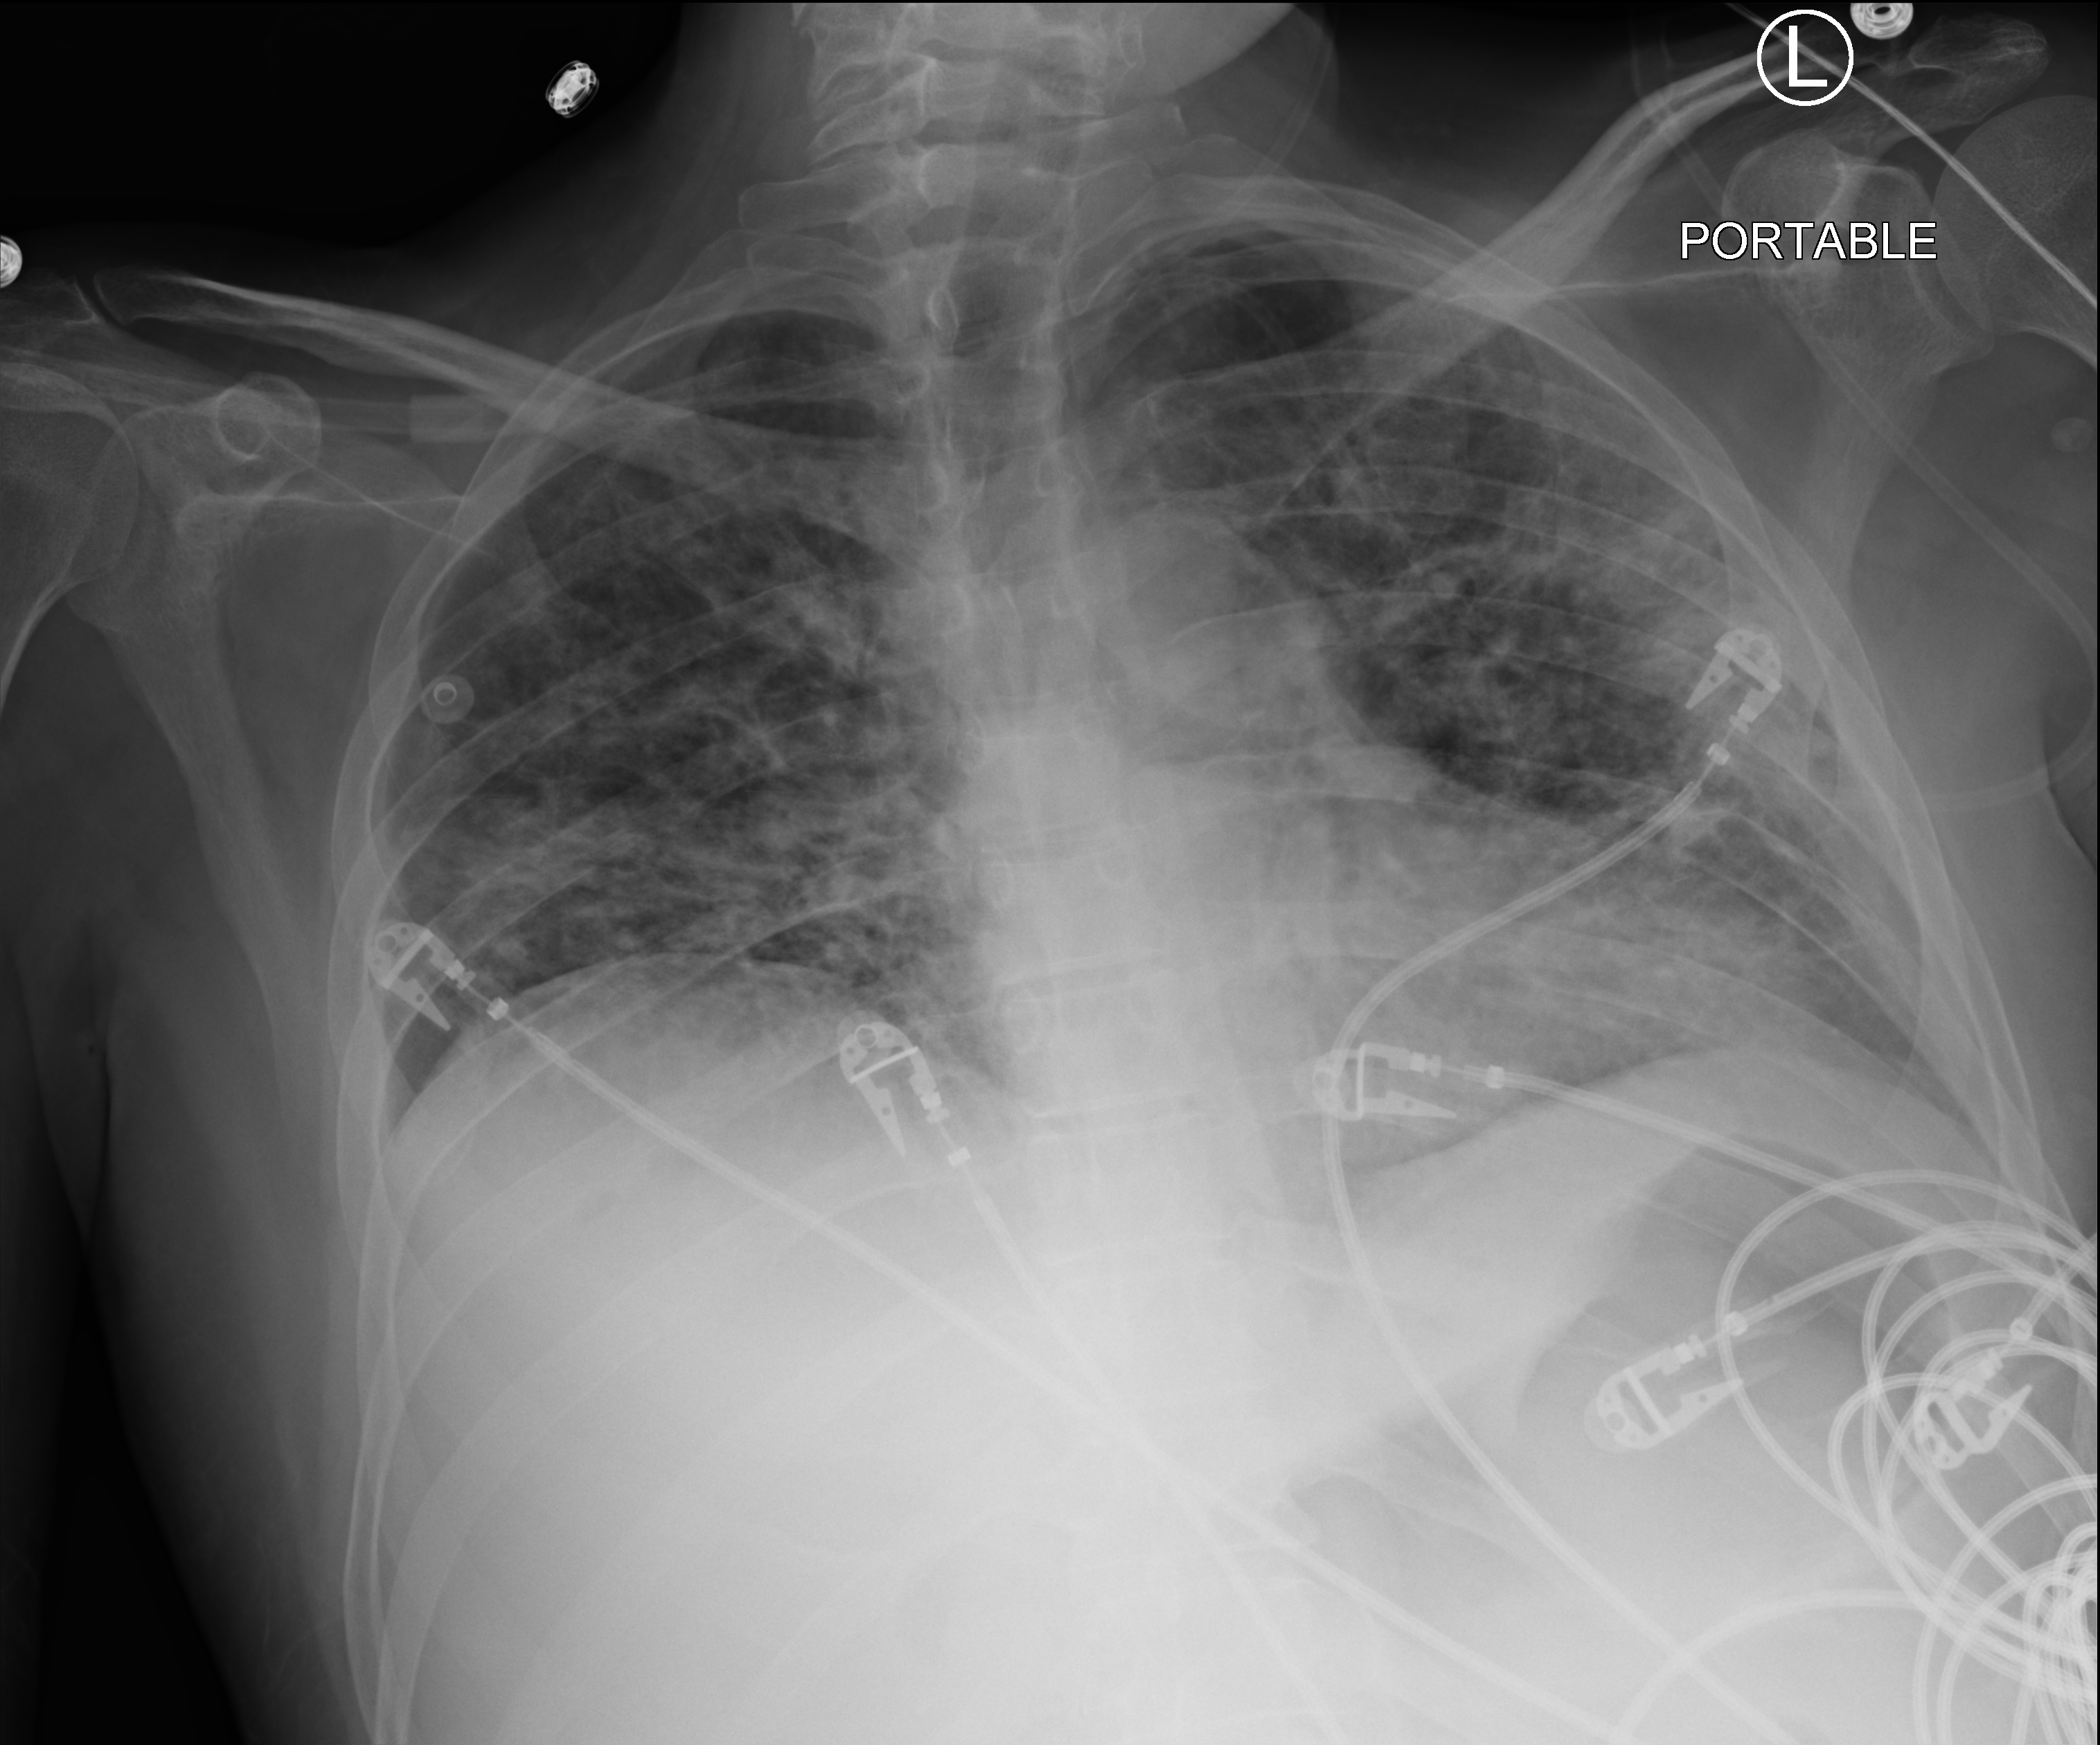
Chest X-ray (portable); anteroposterior (AP) projection. Patient hospitalised with COVID-19; male, aged 18–59 years.
From the hospital-stay record, not from the radiograph (when in the stay this image was taken is not recorded):
- other chronic lung disease (admission record): no
- mechanically ventilated during this hospital stay: yes
- admitted to intensive care during this hospital stay: yes